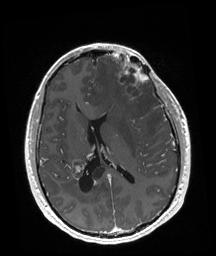
Brain MRI from a brain-tumour surgery series, one axial slice; T1-weighted post-contrast; 216 × 256 image matrix, field of view 219 × 260 mm.
Structures marked on this image (manually delineated by an expert):
- tumour: box from (x=118, y=58) to (x=148, y=103) px